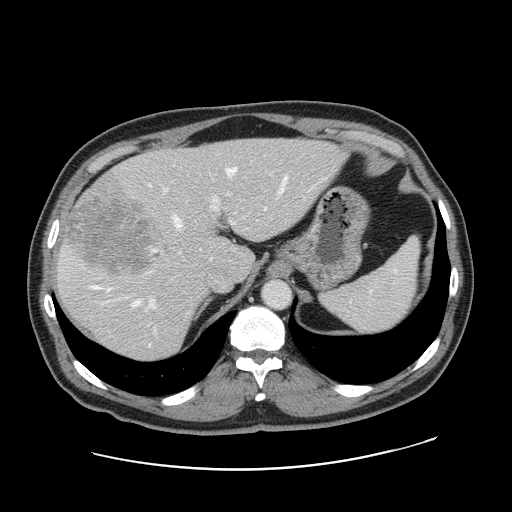
Contrast-enhanced abdominal CT, one axial slice. Position 119 of 178 along the scan axis. 120 kVp. Soft-tissue window (W 400 / L 40 HU). 512 × 512 image matrix, field of view 403 × 403 mm. Male patient, age 63 years. From the clinical record (not read from this slice): diagnosis: colorectal cancer liver metastases, imaged before liver resection; multiple liver metastases: yes; largest metastasis: 8 cm; disease in both lobes: yes.
Outlined on this slice (expert manual segmentation):
- hepatic veins: bounding box [x1, y1, x2, y2] px = [90, 167, 286, 306]
- liver: [56, 139, 343, 361]
- planned liver remnant (the part of the liver to remain after resection): [141, 140, 344, 279]
- portal vein (with intrahepatic branches): [148, 187, 236, 332]
- liver metastasis: [66, 195, 158, 273]